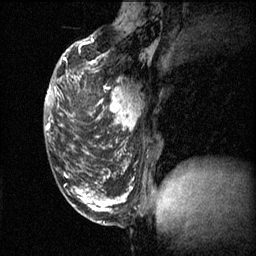
Breast MRI (dynamic contrast-enhanced), one sagittal slice; slice 22 of 60 in the series (ordered by position); 3 images stored at this slice position (order not interpretable as contrast timing); 1.5 T; TE 4.2 ms, TR 11.1 ms; 2 mm slice thickness; 256 × 256 image matrix, field of view 180 × 180 mm. Patient: female, 50 years.
Outlined on this slice (semi-automatic segmentation, software-assisted and operator-edited):
- analysis volume of interest (the breast-tissue region the enhancement analysis was run in; not a lesion): bounding box <70,68,142,141> (left, top, right, bottom; pixels)
- tumour enhancement mask (voxels above the 70 % enhancement threshold inside the analysis volume of interest): <71,68,139,139>